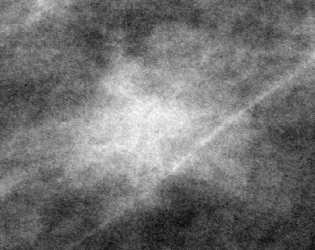
Region of interest cut from a scanned film mammogram (one marked finding), left breast, CC view.
Marked abnormality: mass, shape irregular, margins microlobulated; BI-RADS assessment category 3; subtlety rating 5 on a 1 (subtle) to 5 (obvious) scale; benign; no additional work-up was recommended (benign without callback).